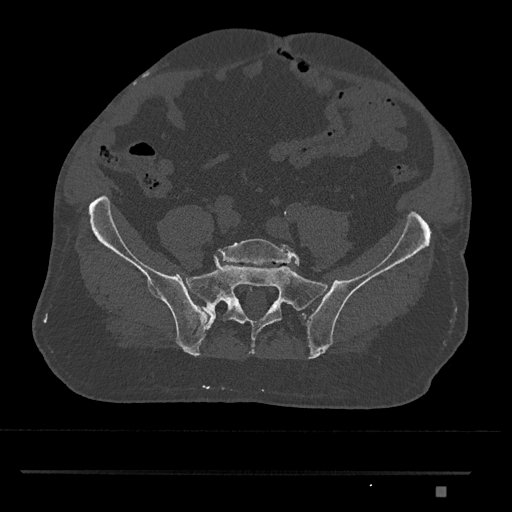
CT including the spine, one axial slice; slice 512 of 1134 in the series (ordered by position); reconstruction kernel Br40s/3; bone window (W 1800 / L 400 HU); 0.5 mm slice thickness; 512 × 512 image matrix. Patient: male, 65 years. Case-level facts recorded for this patient, not image findings: primary cancer: prostate.
Structures marked on this image (semi-automatically segmented with operator editing):
- L5 vertebra: bounding box (x1, y1, x2, y2) in pixels: (216, 238, 300, 266)